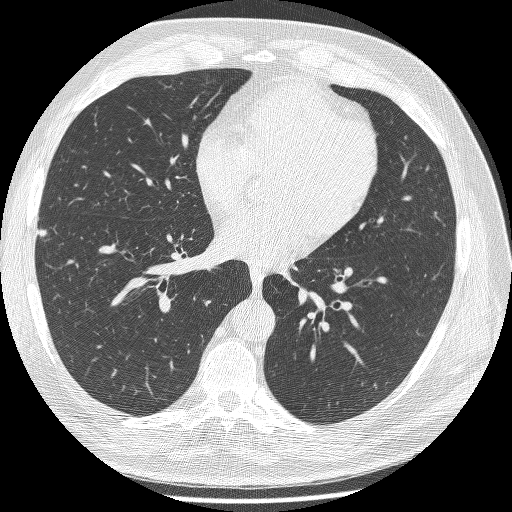
Low-dose screening chest CT, one axial slice; slice 108 of 241 in the series (ordered by position); reconstruction kernel BONE; lung window (W 1500 / L -600 HU); 512 × 512 image matrix, field of view 346 × 346 mm.
Annotated regions visible in this slice (manually delineated by an expert):
- lesion 1 (tumor, lower lobe of right lung): bounding box <38,229,47,237> (left, top, right, bottom; pixels)